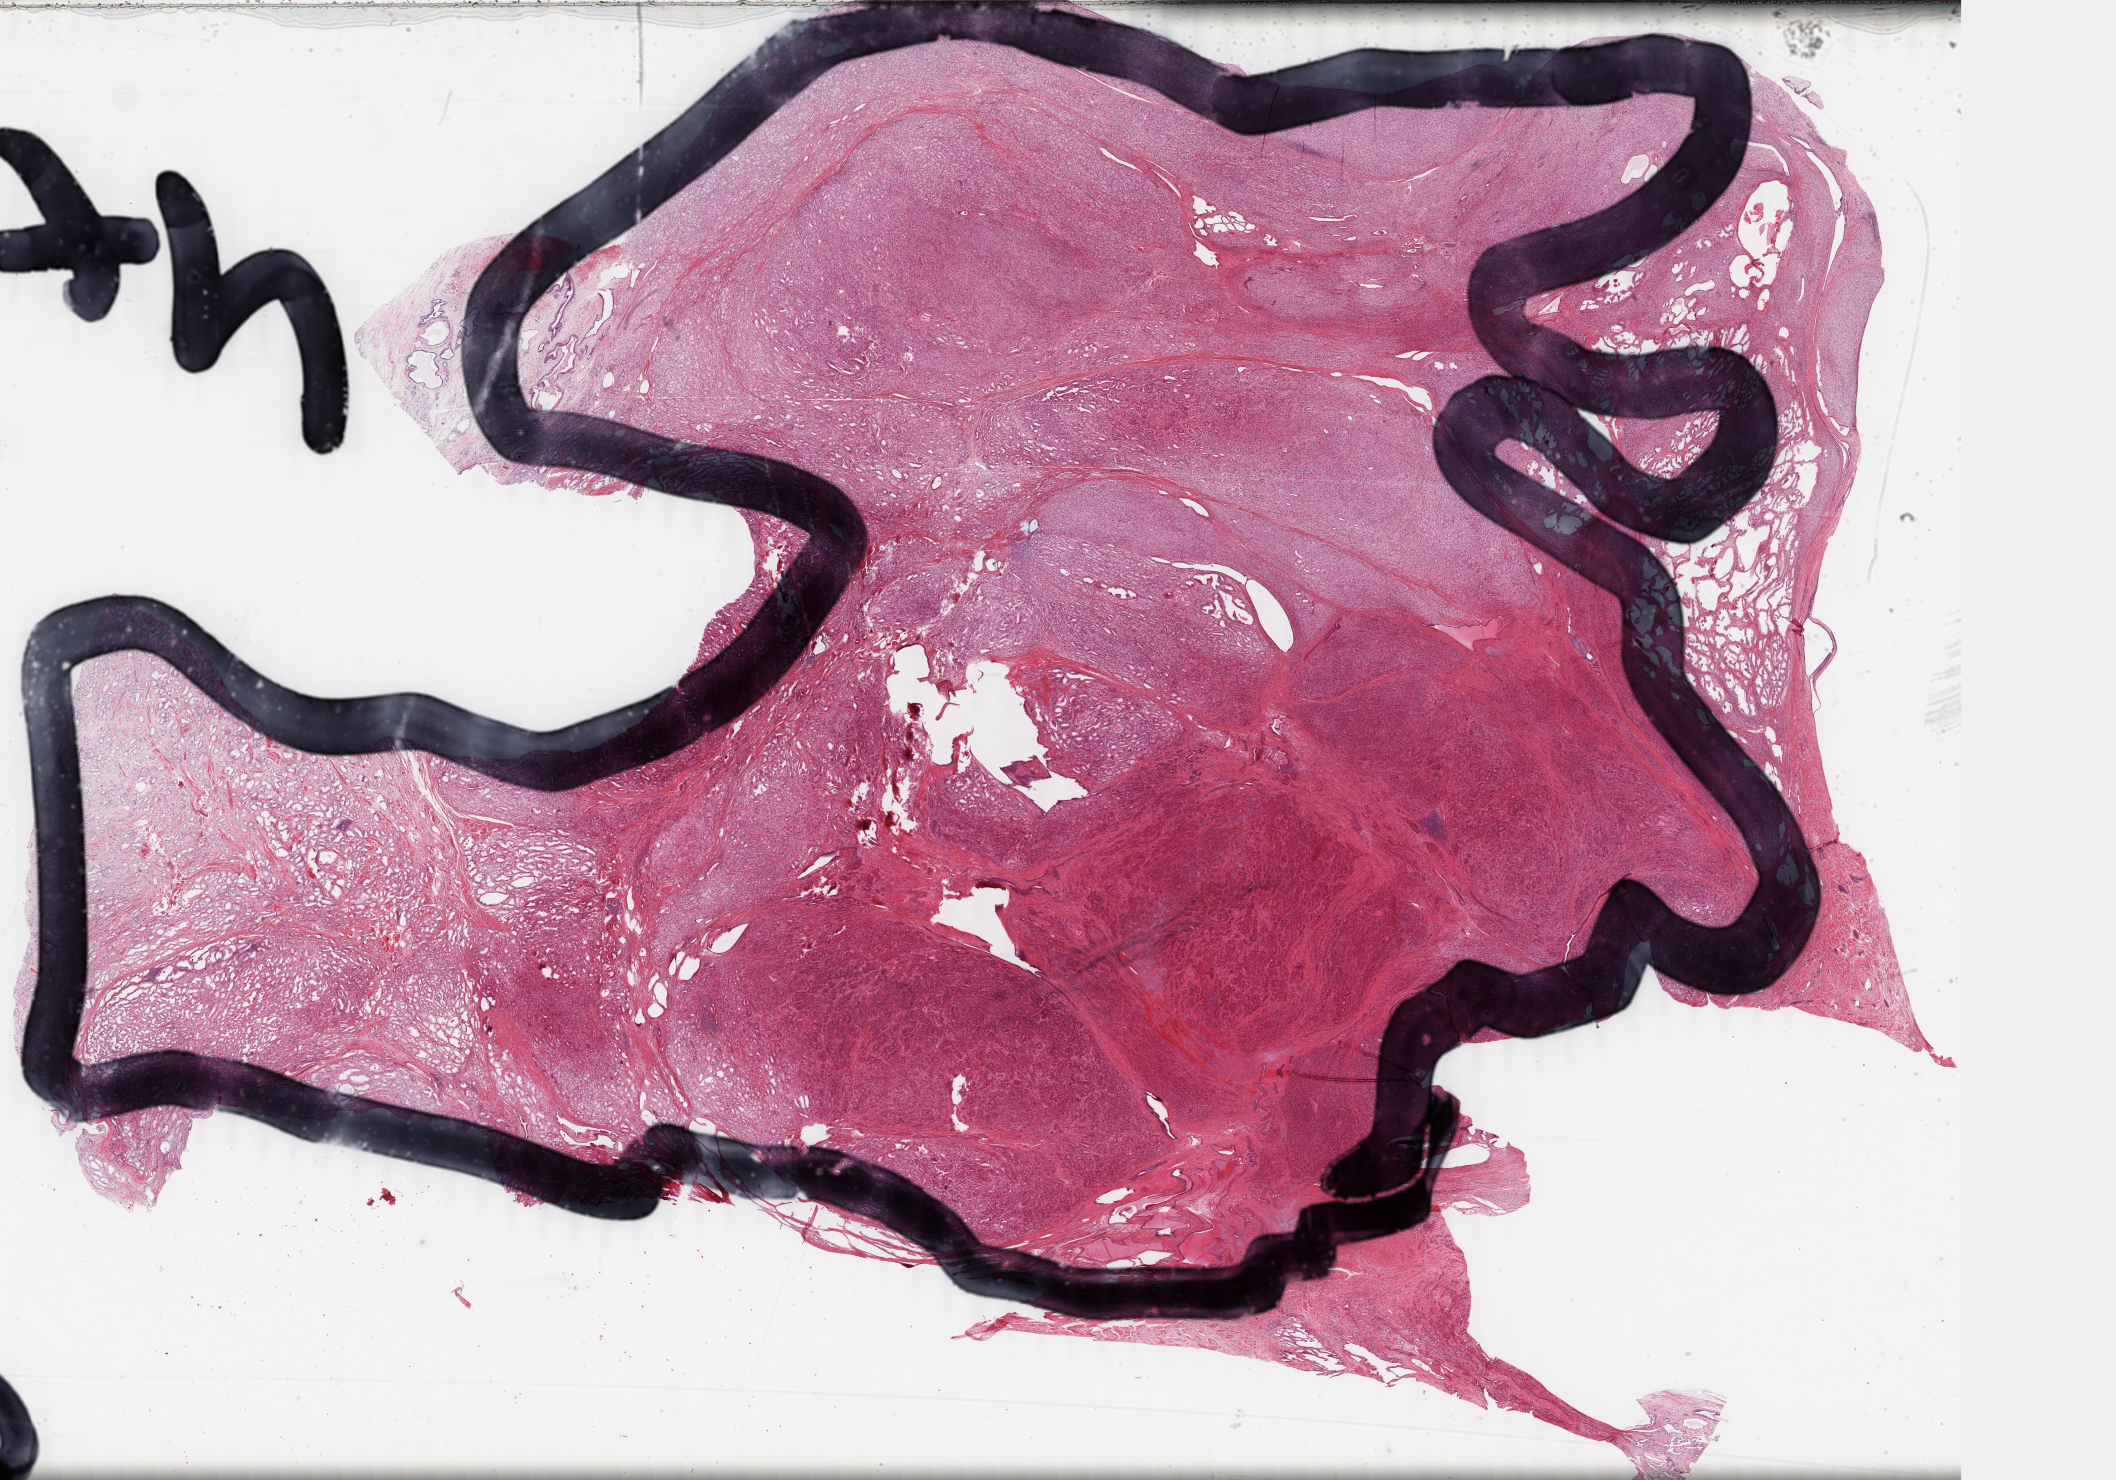
H&E whole-slide image, a low-resolution overview of the entire scanned area, about 33.7 x 23.5 mm. Formalin-fixed paraffin-embedded (FFPE) diagnostic section. Sample: primary tumour, prostate. Male patient; age at initial diagnosis 67 years. Gleason score: 7 (4+3).
- pathologic diagnosis: Adenocarcinoma, NOS (prostate gland)
- lymph nodes positive (case pathology): 0 of 18 examined